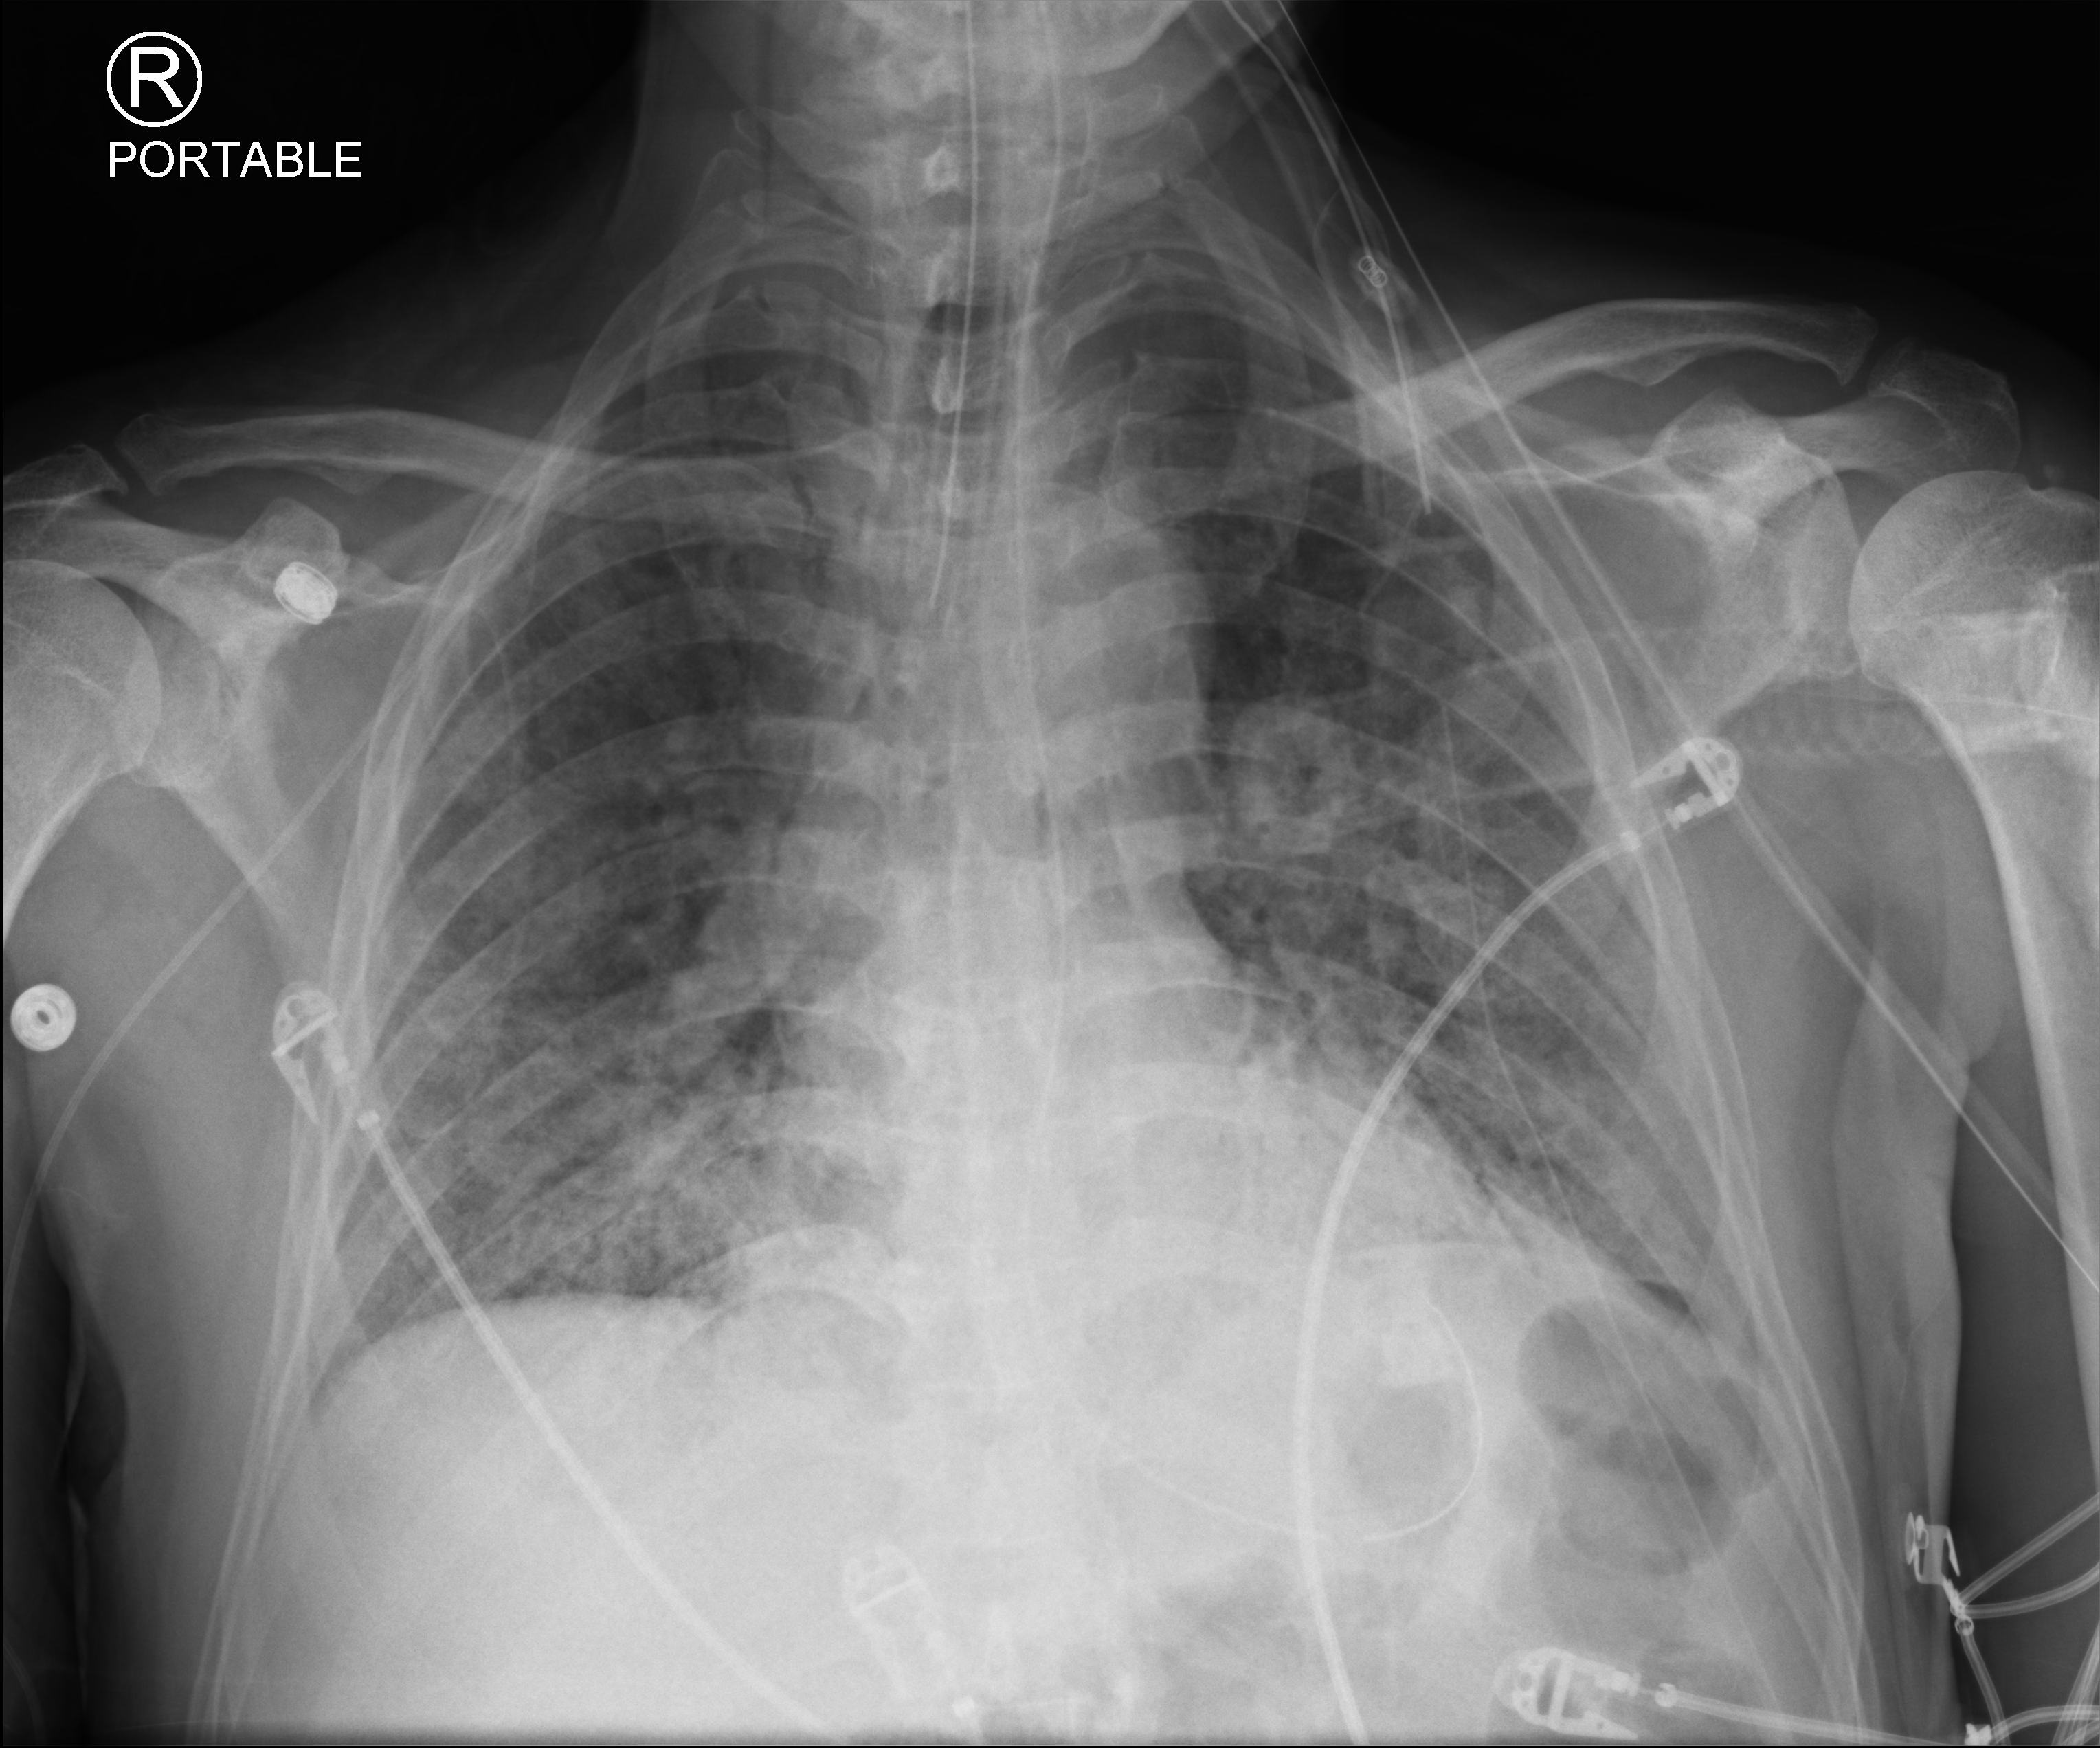
Portable chest radiograph, anteroposterior (AP) projection. Male patient hospitalised with COVID-19, age 60–74 years.
Admission-level facts for this patient (not findings on this image; timing relative to this image not recorded): other chronic lung disease (admission record): no; length of hospital stay: 37 days; mechanically ventilated during this hospital stay: yes.